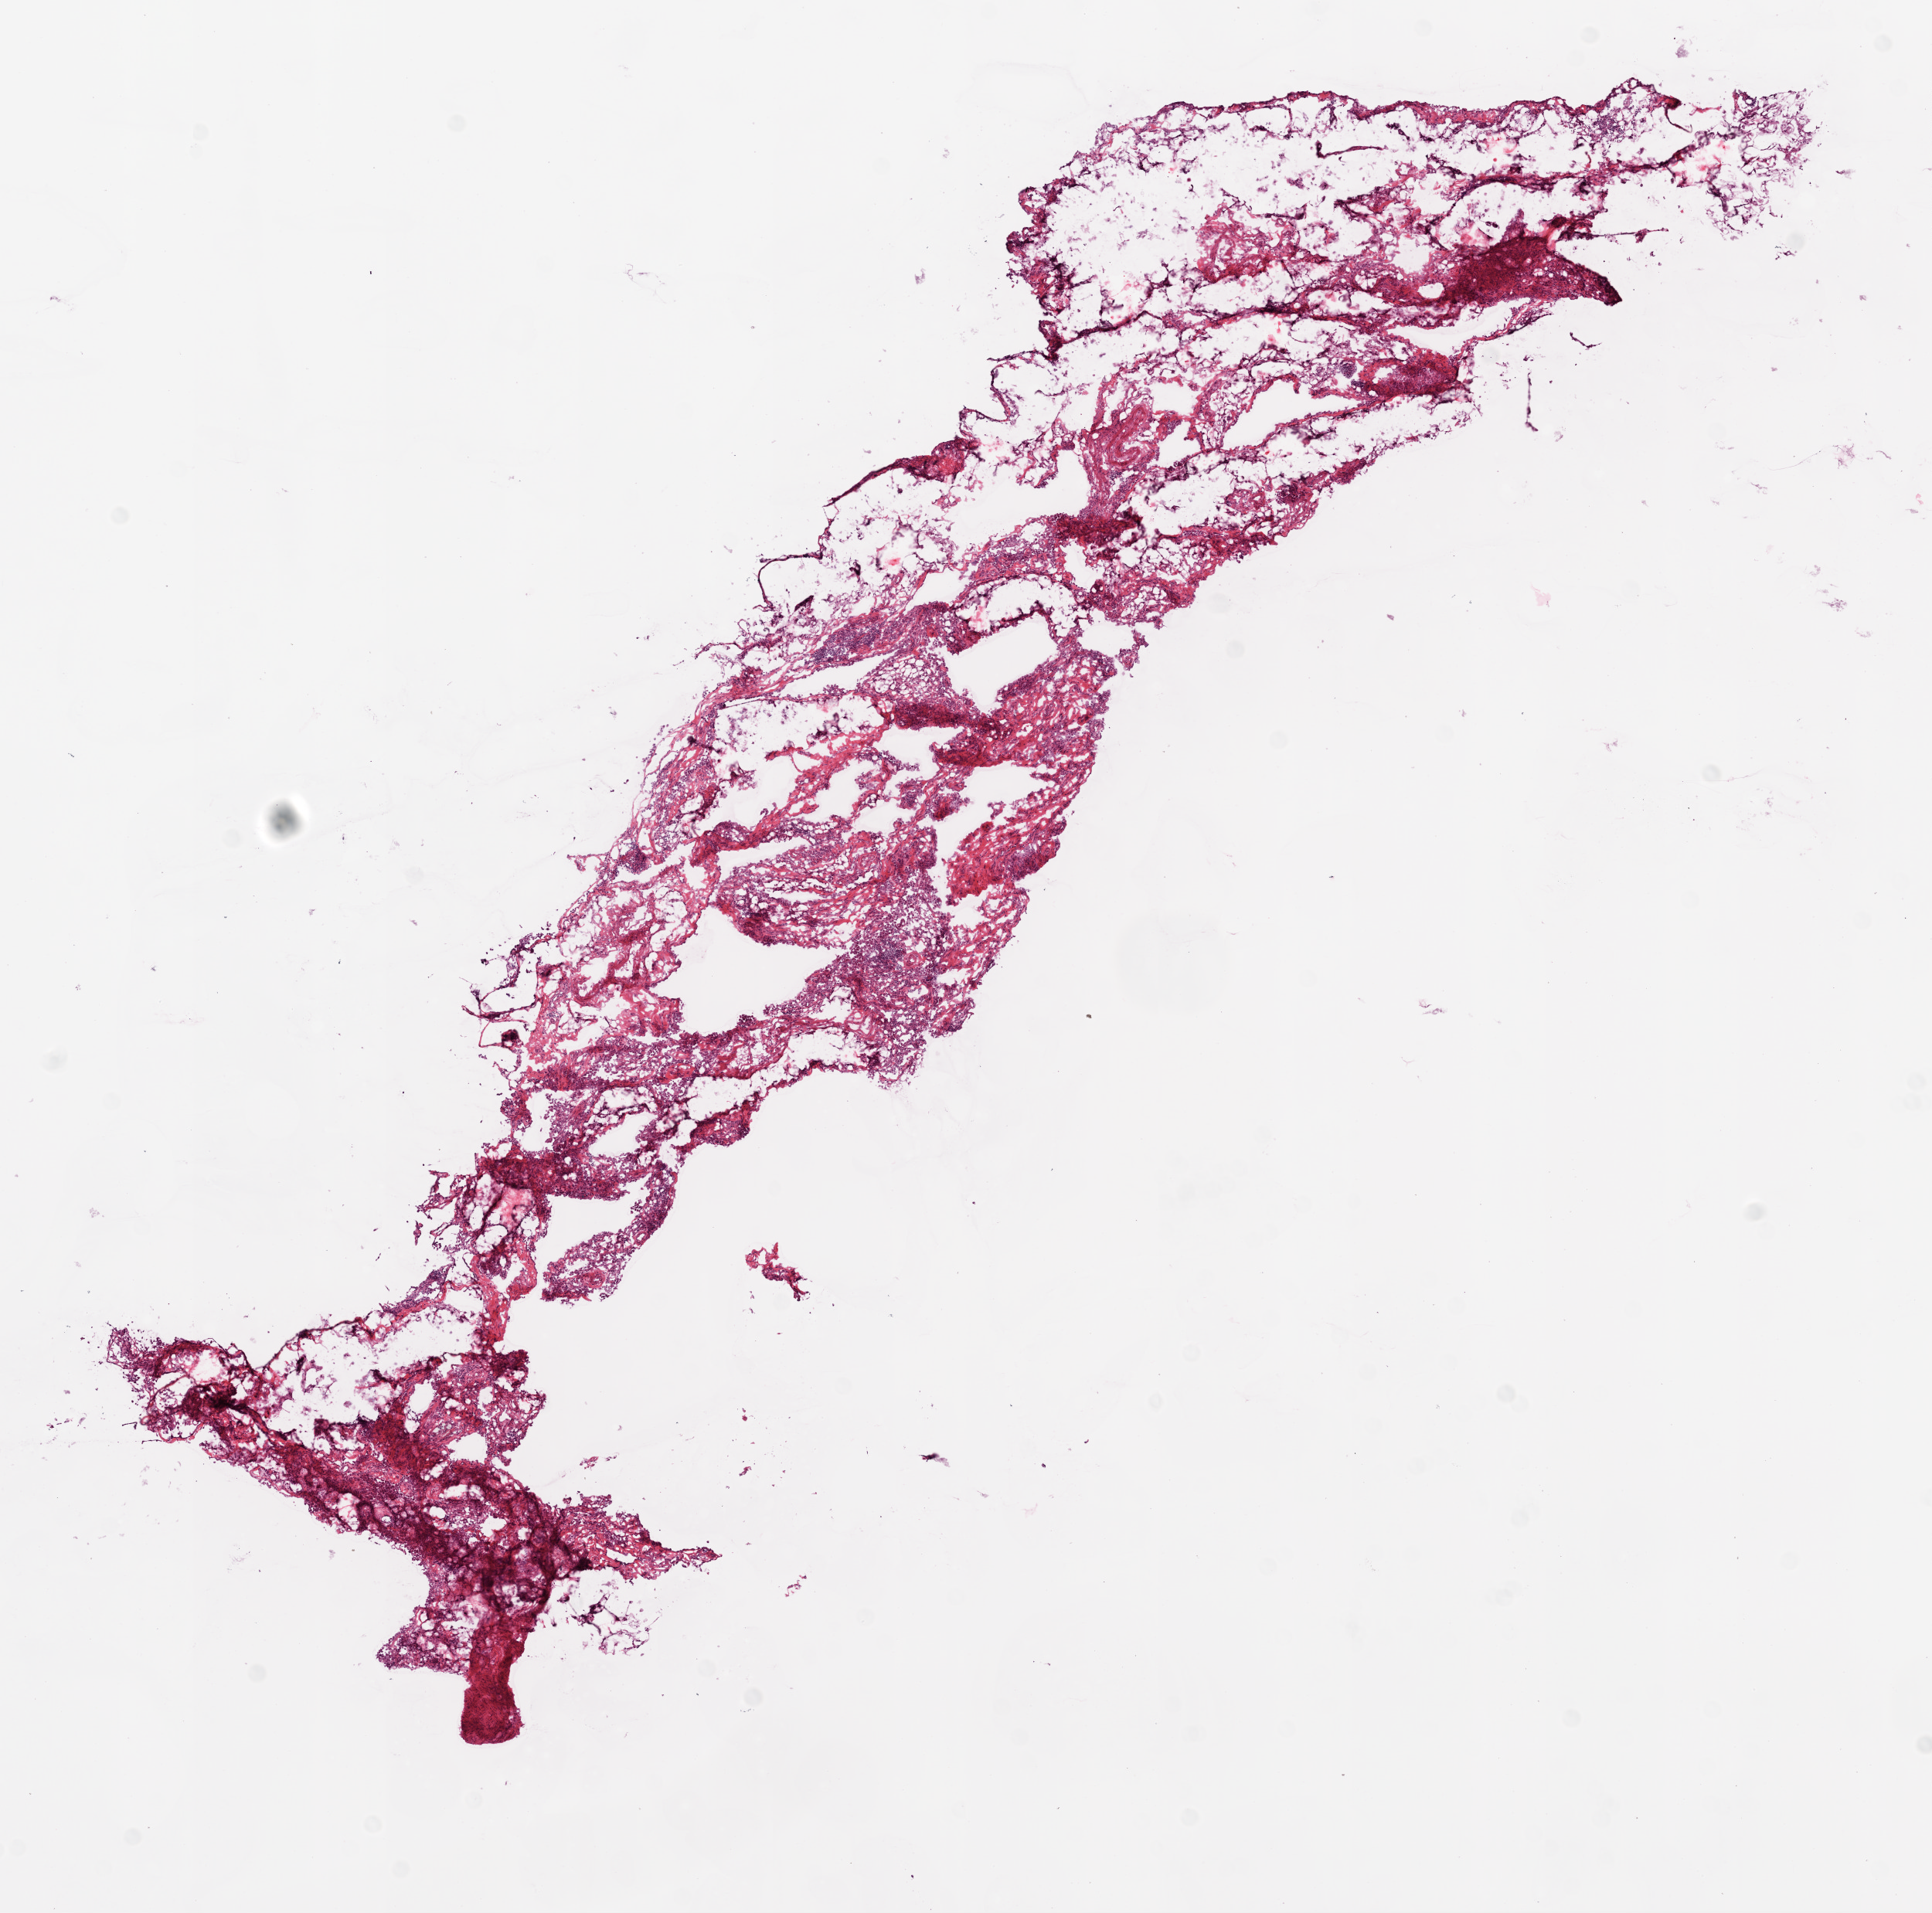
Whole-slide histology image, H&E-stained, low-resolution overview of the scanned area, about 10.0 x 9.9 mm (acquisition: 20x scan); frozen section; solid tissue normal (non-tumour tissue) sample from the ovary. Female patient; age at initial diagnosis 69 years.
This section: solid tissue normal (non-tumour) sample from the same patient. Patient diagnosis: Serous cystadenocarcinoma, NOS.